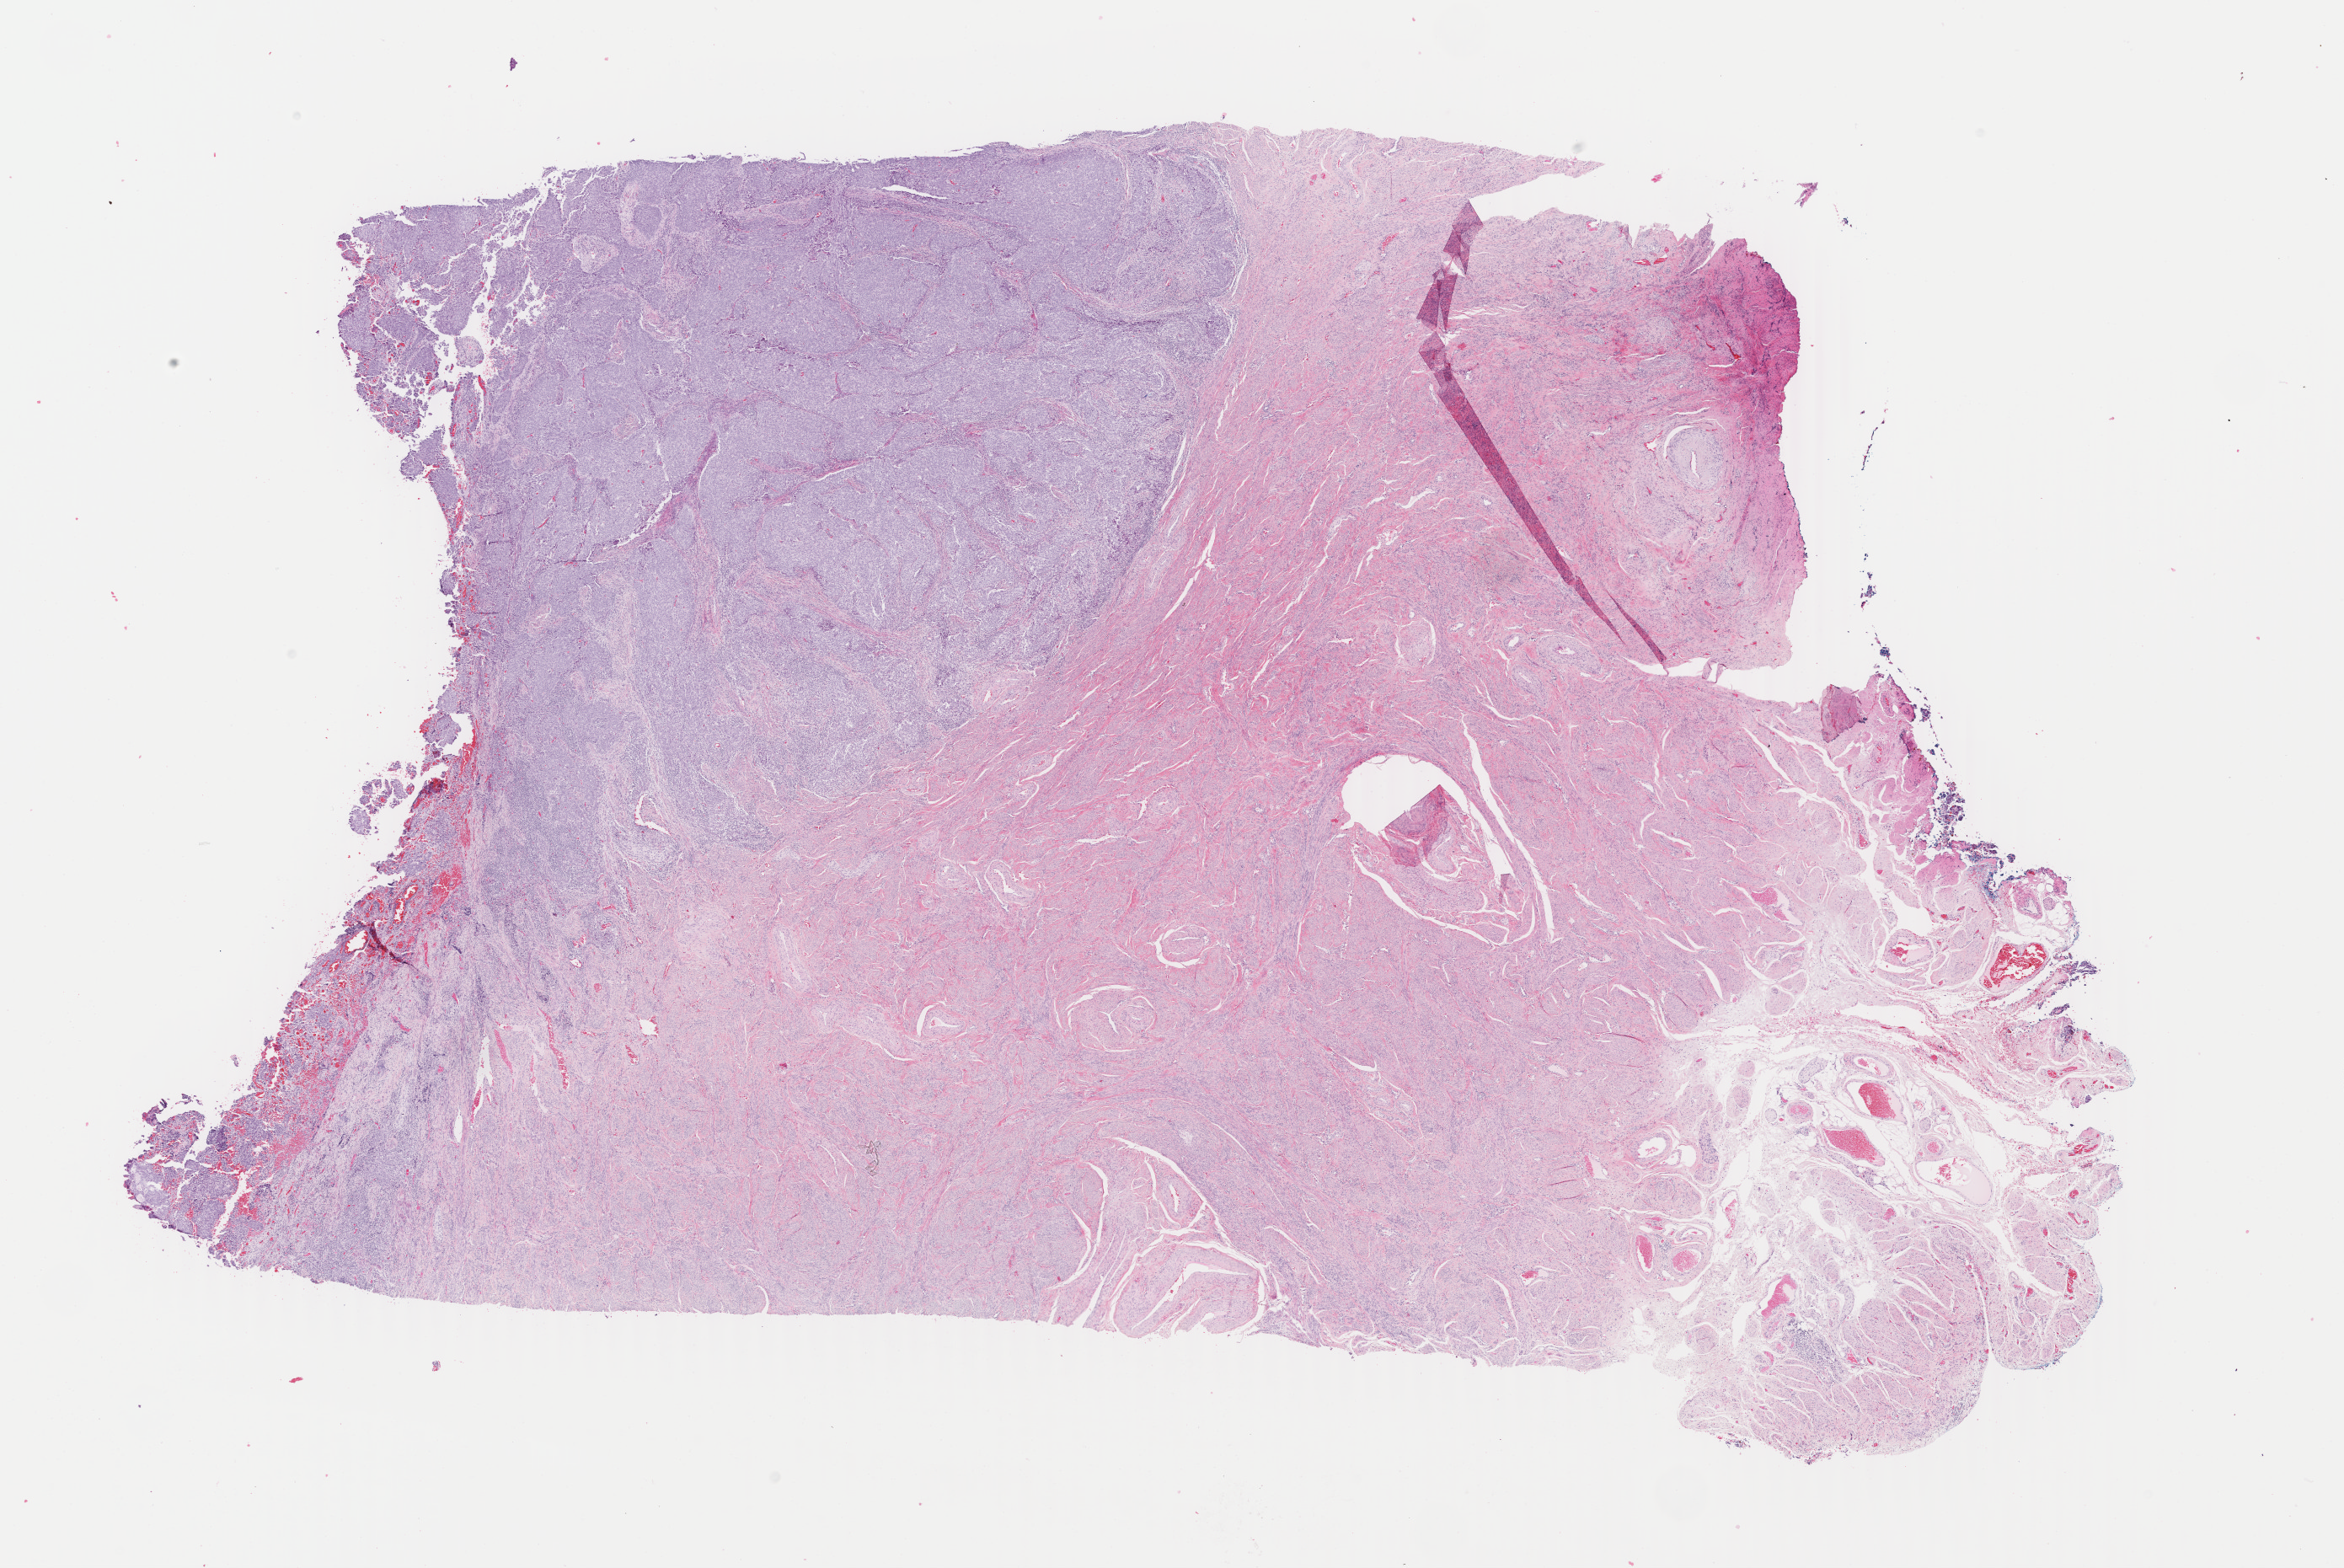
Whole-slide histology image, Hematoxylin and eosin (H&E) stained — low-resolution overview of the scanned area, about 22.1 x 14.8 mm (slide scanned at 40x), formalin-fixed paraffin-embedded (FFPE) diagnostic section, sample: primary tumour, uterus. Female patient; age at initial diagnosis 51 years. Histologic grade: G3 (poorly differentiated).
FIGO stage: II. Lymph nodes positive (case pathology): 0 of 6 examined. Histologic diagnosis: Endometrioid adenocarcinoma, NOS (endometrium).